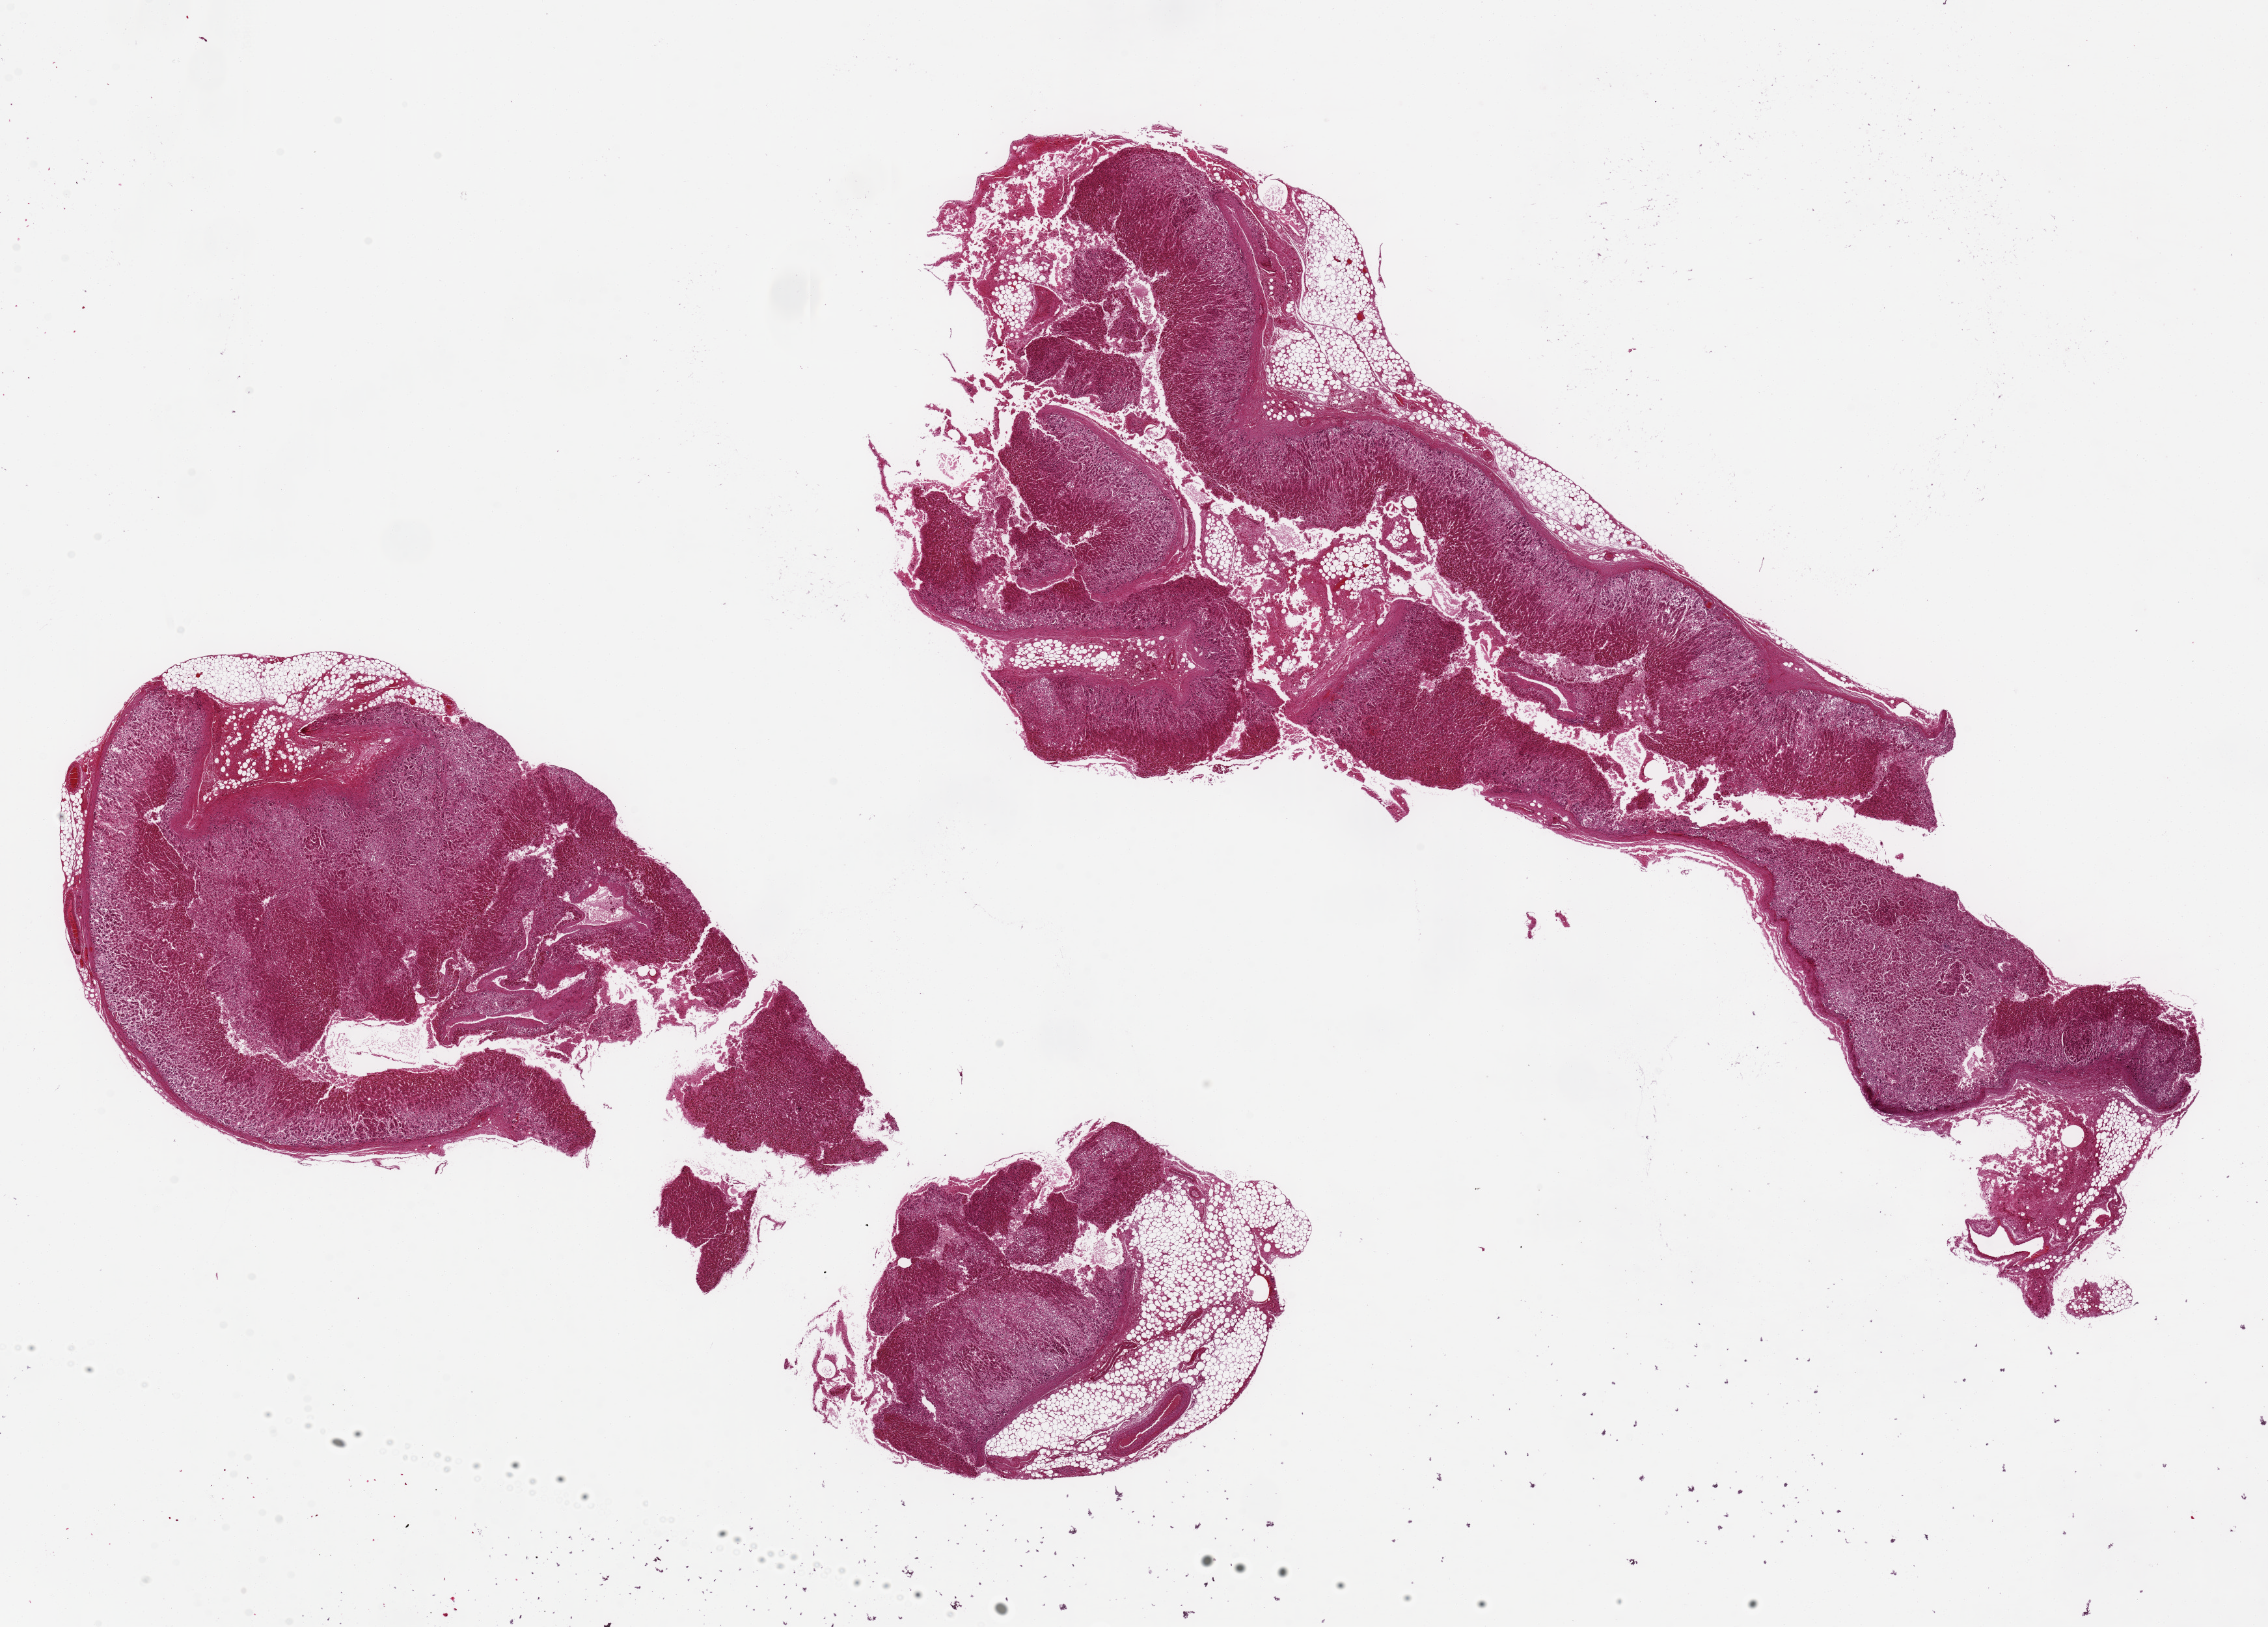
Digitized hematoxylin and eosin (H&E)-stained section — shown as a low-resolution overview of the whole scanned area (about 27.6 x 19.8 mm); PAXgene-fixed paraffin-embedded (PFPE) section; section of adrenal gland (target tissue); tissue donor sample. Donor sex: male.
Review note (as recorded): 2 aliquots, ~15x8mm. ~30% adherment/interstital fat.